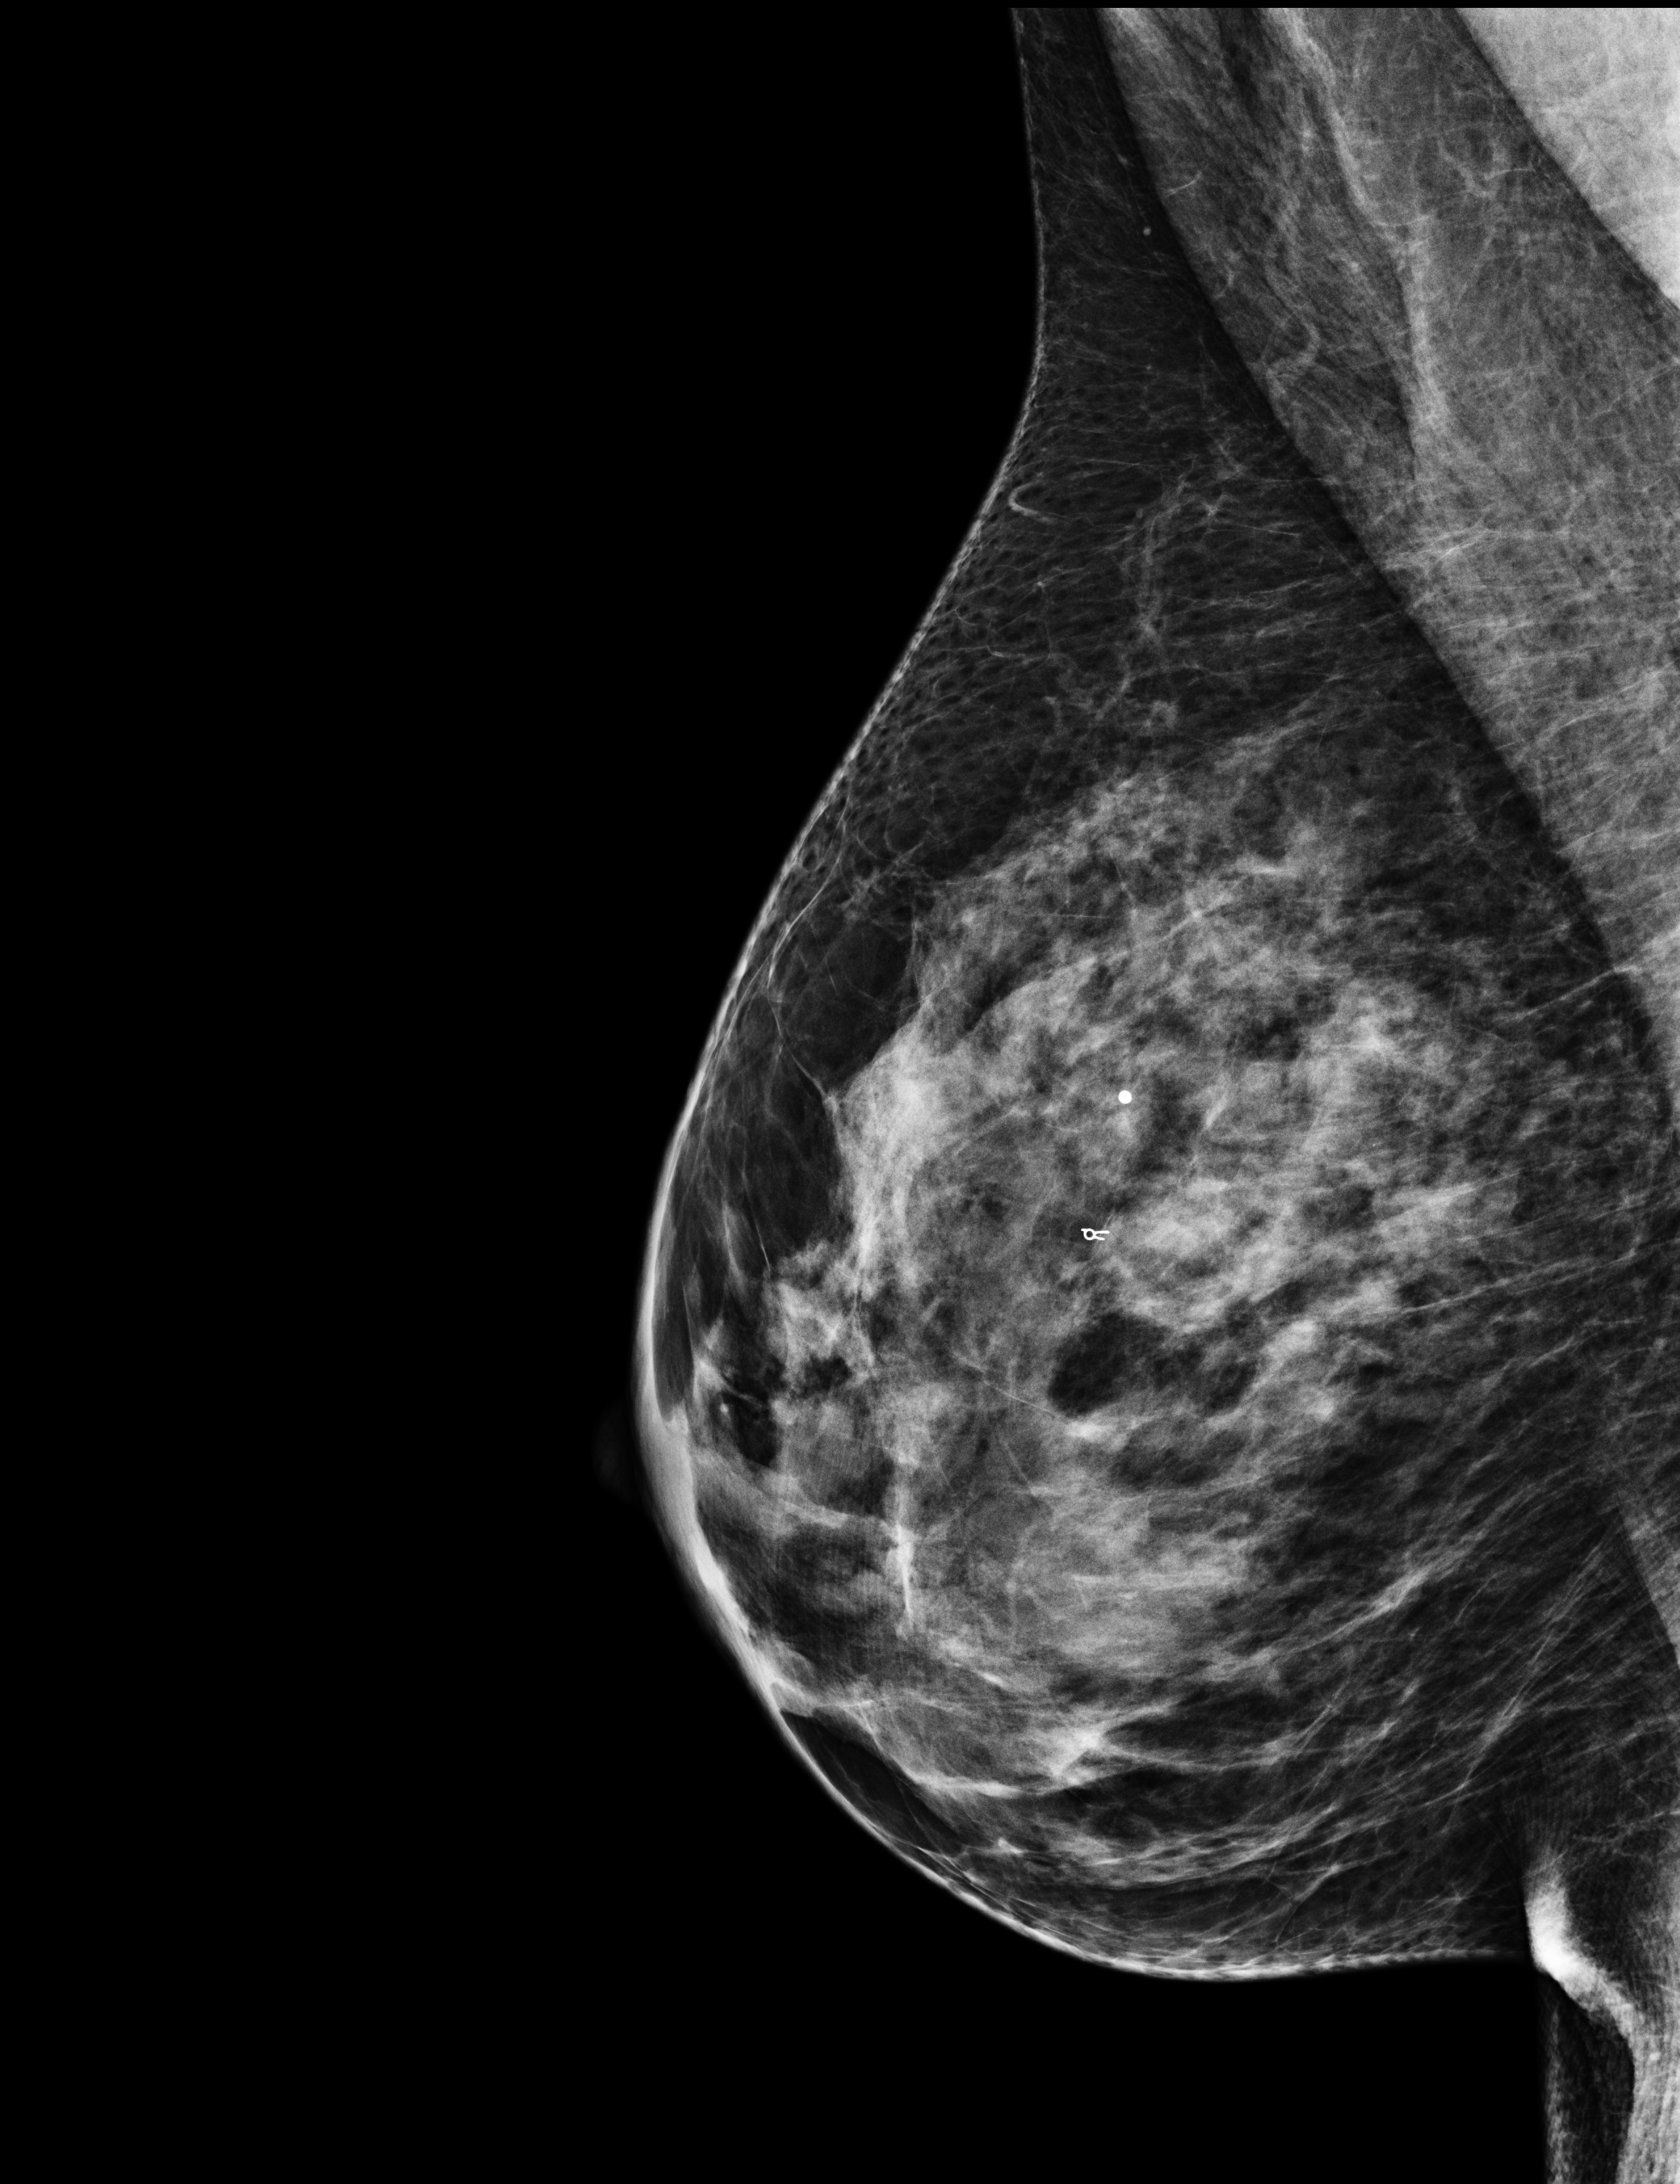
Full-field digital mammogram (FFDM); right breast; medio-lateral oblique projection; screening examination; compressed breast thickness 49 mm; system: Selenia Dimensions. Female patient, age 62 years.
- BI-RADS breast density category at the screening exam (both breasts, scale 1–4): 3
- final BI-RADS category for the screening round (tomosynthesis exam, both breasts): category 2
- recall: no recall after this screen